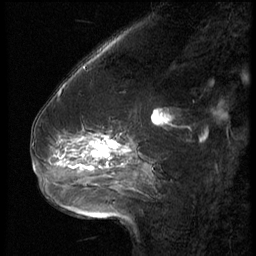
Breast MRI (dynamic contrast-enhanced), one sagittal slice; slice 21 of 62 in the series (ordered by position); 3 images stored at this slice position (order not interpretable as contrast timing); 1.5 T; TE 4.2 ms, TR 9 ms; 2.5 mm slice thickness; 256 × 256 image matrix, field of view 180 × 180 mm. Female patient, age 54 years. From the clinical record (not read from this slice): setting: breast cancer imaged before/during neoadjuvant chemotherapy; receptor status: HR-positive, HER2-negative.
Annotated regions visible in this slice (semi-automatic segmentation, software-assisted and operator-edited):
- analysis volume of interest (the breast-tissue region the enhancement analysis was run in; not a lesion): bounding box <42,126,146,183> (left, top, right, bottom; pixels)
- tumour enhancement mask (voxels above the 140 % enhancement threshold inside the analysis volume of interest): <90,134,127,169>